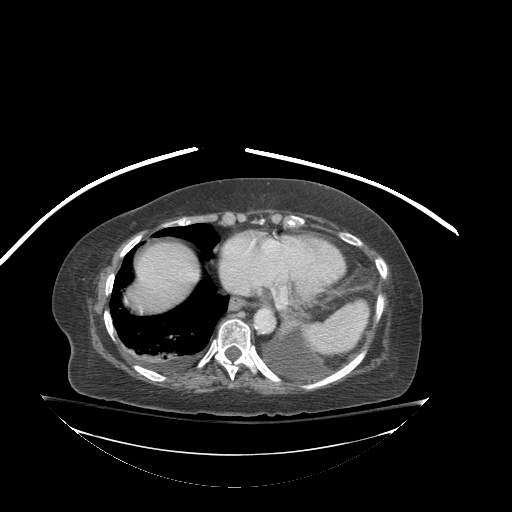
Contrast-enhanced abdominal CT (liver protocol), one axial slice. 140 kVp. Soft-tissue window (W 400 / L 40 HU). 2.5 mm slice thickness. 512 × 512 image matrix. Case-level facts recorded for this patient, not image findings: diagnosis: hepatocellular carcinoma (patient treated with transarterial chemoembolisation; whether this scan precedes or follows treatment is not stated here); TNM stage (as recorded): Stage-I; Child-Pugh class: B; tumour differentiation: well-moderately differentiated; tumour nodularity: uninodular.
Structures marked on this image (semi-automatically segmented with operator editing):
- liver parenchyma outside the tumour (the mass and vessels are separate outlines, so this box may not span the whole liver): bounding box (x1, y1, x2, y2) in pixels: (128, 242, 198, 312)
- liver vessels: (187, 273, 194, 277)